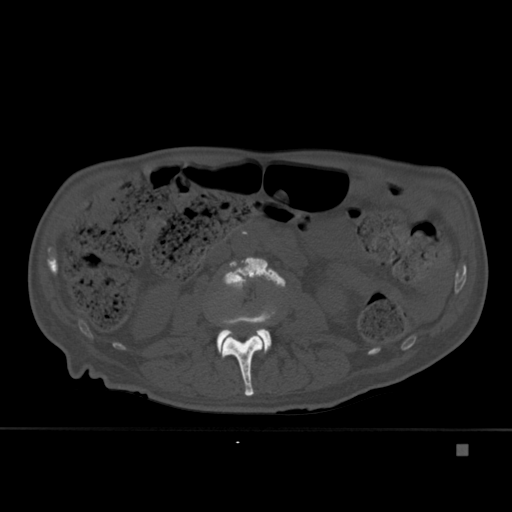
CT including the spine, one axial slice; position 154 of 451 along the scan axis; bone window (W 1800 / L 400 HU); 1.5 mm slice thickness; 512 × 512 image matrix, field of view 378 × 378 mm. Patient: male, 75 years. Case-level facts recorded for this patient, not image findings: primary cancer: prostate.
Structures marked on this image (semi-automatic segmentation, software-assisted and operator-edited):
- L2 vertebra: bounding box <221,311,275,396> (left, top, right, bottom; pixels)
- L3 vertebra: <219,257,286,354>